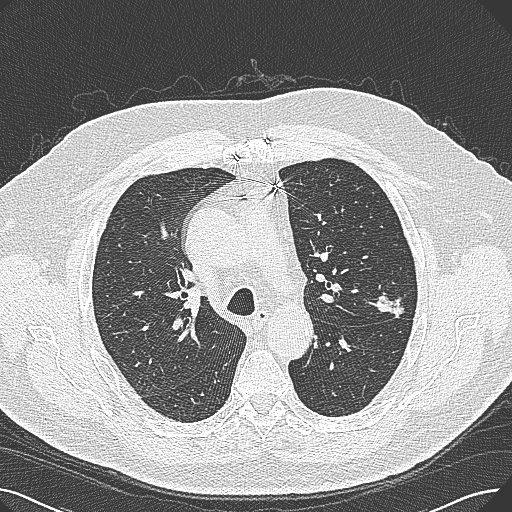
Chest CT (low-dose screening protocol), one axial image. First (baseline) screen. Lung window (W 1500 / L -600 HU). 1 mm slice thickness. Slice 93 of 269 in the series. 512 × 512 image matrix. Male, age 74 years at enrolment. Former smoker at enrolment.
Lesion marked by an expert reader, bounding box [x1, y1, x2, y2] px = [366, 274, 427, 326]. The exam's reader record, not a measurement of the box and not confirmed to be the same lesion: non-calcified nodule or mass ≥4 mm, left upper lobe, 15 × 10 mm, poorly defined margins, soft tissue attenuation. Lung cancer was diagnosed 124 days after this screen: adenocarcinoma, NOS, left upper lobe, well differentiated (G1), stage IA (AJCC 6th edition), 26 mm at pathology.